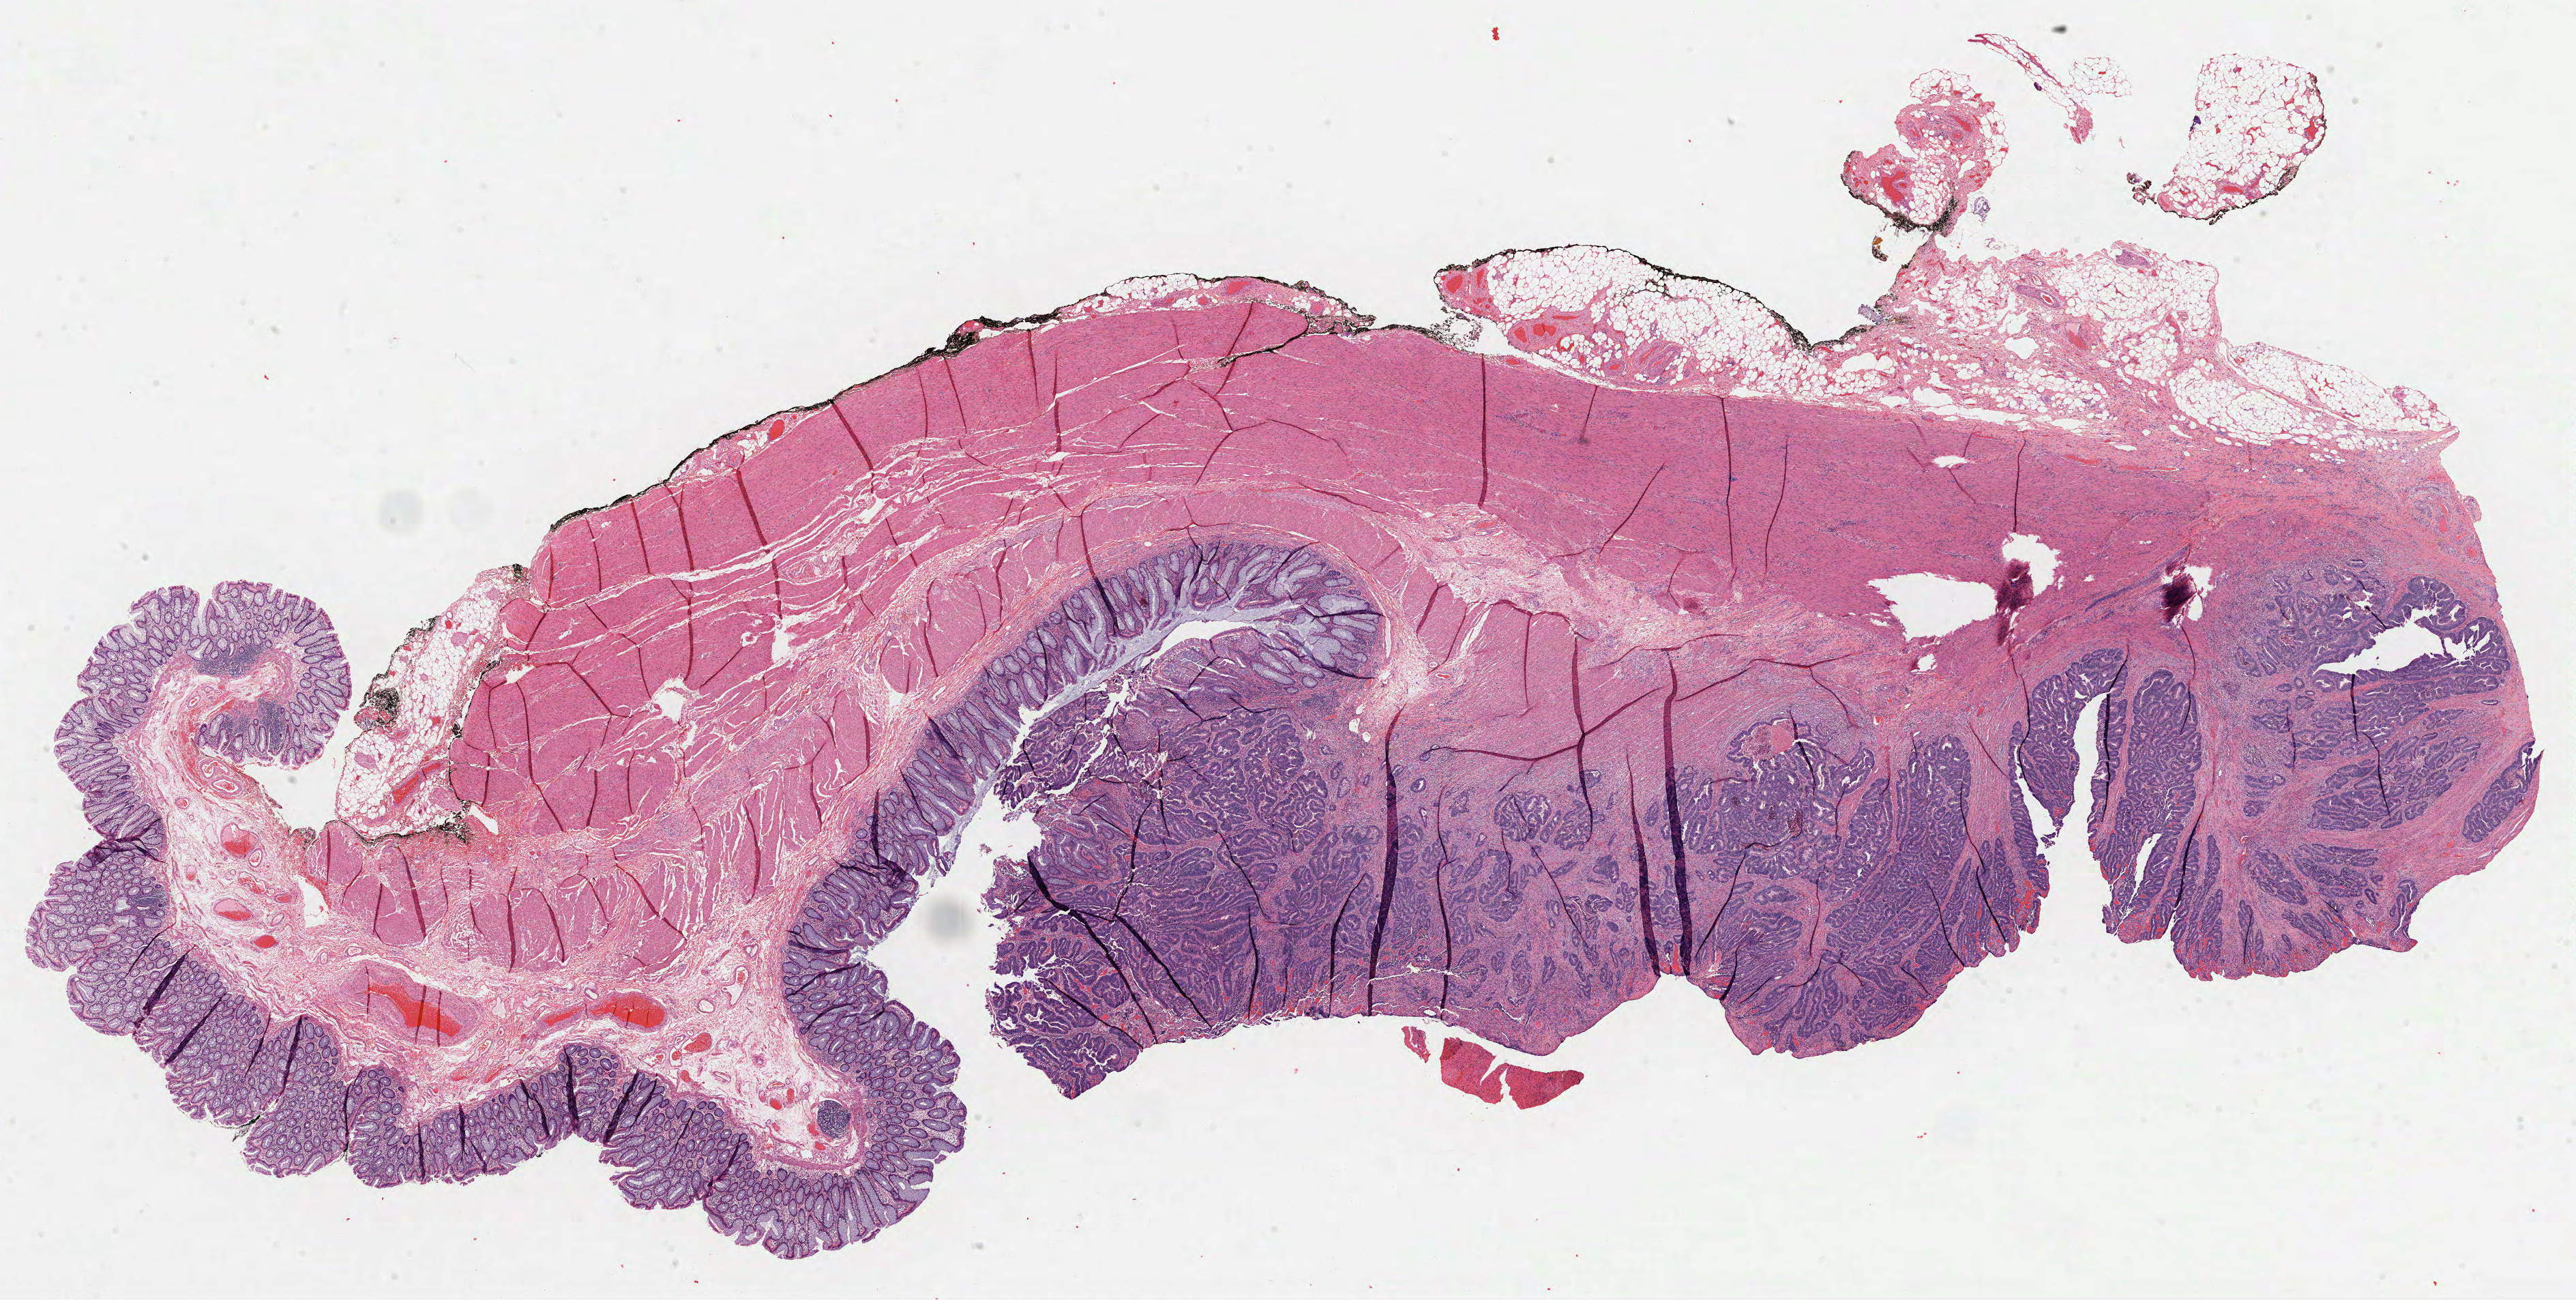
H&E-stained whole-slide image — whole scanned area (about 30.5 x 15.4 mm, slide scanned at 40x) shown as a low-resolution overview. FFPE section. Sample: primary tumour, rectum. Patient: female, age at initial diagnosis 79 years.
Histologic diagnosis: Adenocarcinoma, NOS. Lymph nodes positive (case pathology): 2 of 14 examined.